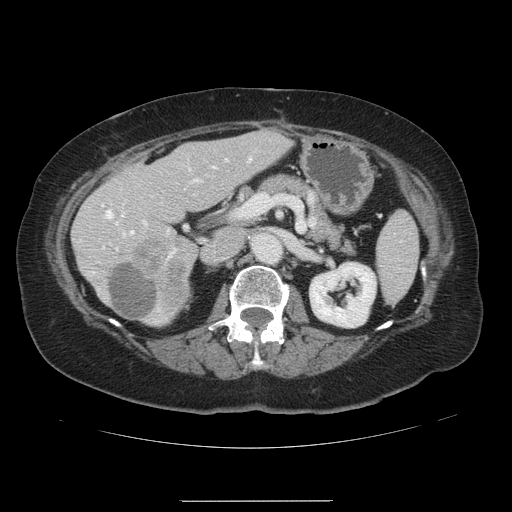
Contrast-enhanced abdominal CT, one axial slice. Position 62 of 141 along the scan axis. Intravenous contrast given. Soft-tissue window (W 400 / L 40 HU). 512 × 512 image matrix. Female patient, age 74 years. From the clinical record (not read from this slice): diagnosis: colorectal cancer liver metastases, imaged before liver resection; multiple liver metastases: yes; largest metastasis: 7 cm.
Annotated regions visible in this slice (manually delineated by an expert):
- hepatic veins: bounding box (x1, y1, x2, y2) in pixels: (105, 210, 135, 235)
- liver: (72, 131, 290, 326)
- planned liver remnant (the part of the liver to remain after resection): (72, 131, 290, 324)
- portal vein (with intrahepatic branches): (116, 158, 251, 256)
- liver metastasis: (109, 264, 159, 320)
- liver metastasis: (130, 240, 189, 310)